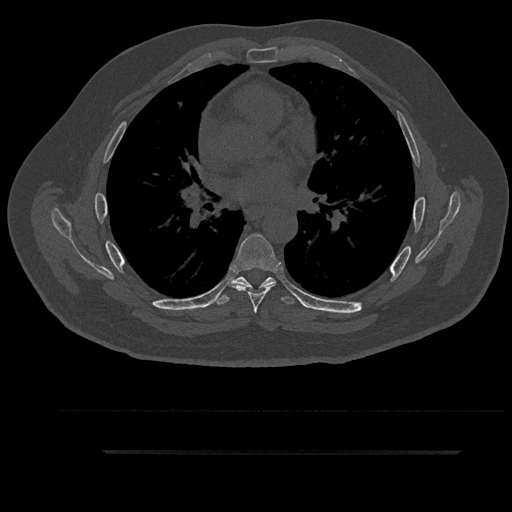
CT including the spine, one axial slice. Position 561 of 797 along the scan axis. 120 kVp. Bone window (W 1800 / L 400 HU). 0.5 mm slice thickness. 512 × 512 image matrix, field of view 432 × 432 mm. Patient: male, 63 years. Case-level facts recorded for this patient, not image findings: primary cancer: renal.
Structures marked on this image (semi-automatically segmented with operator editing):
- T5 vertebra: bounding box (x1, y1, x2, y2) in pixels: (246, 277, 271, 291)
- T6 vertebra: (231, 234, 281, 313)
- T7 vertebra: (216, 277, 298, 305)